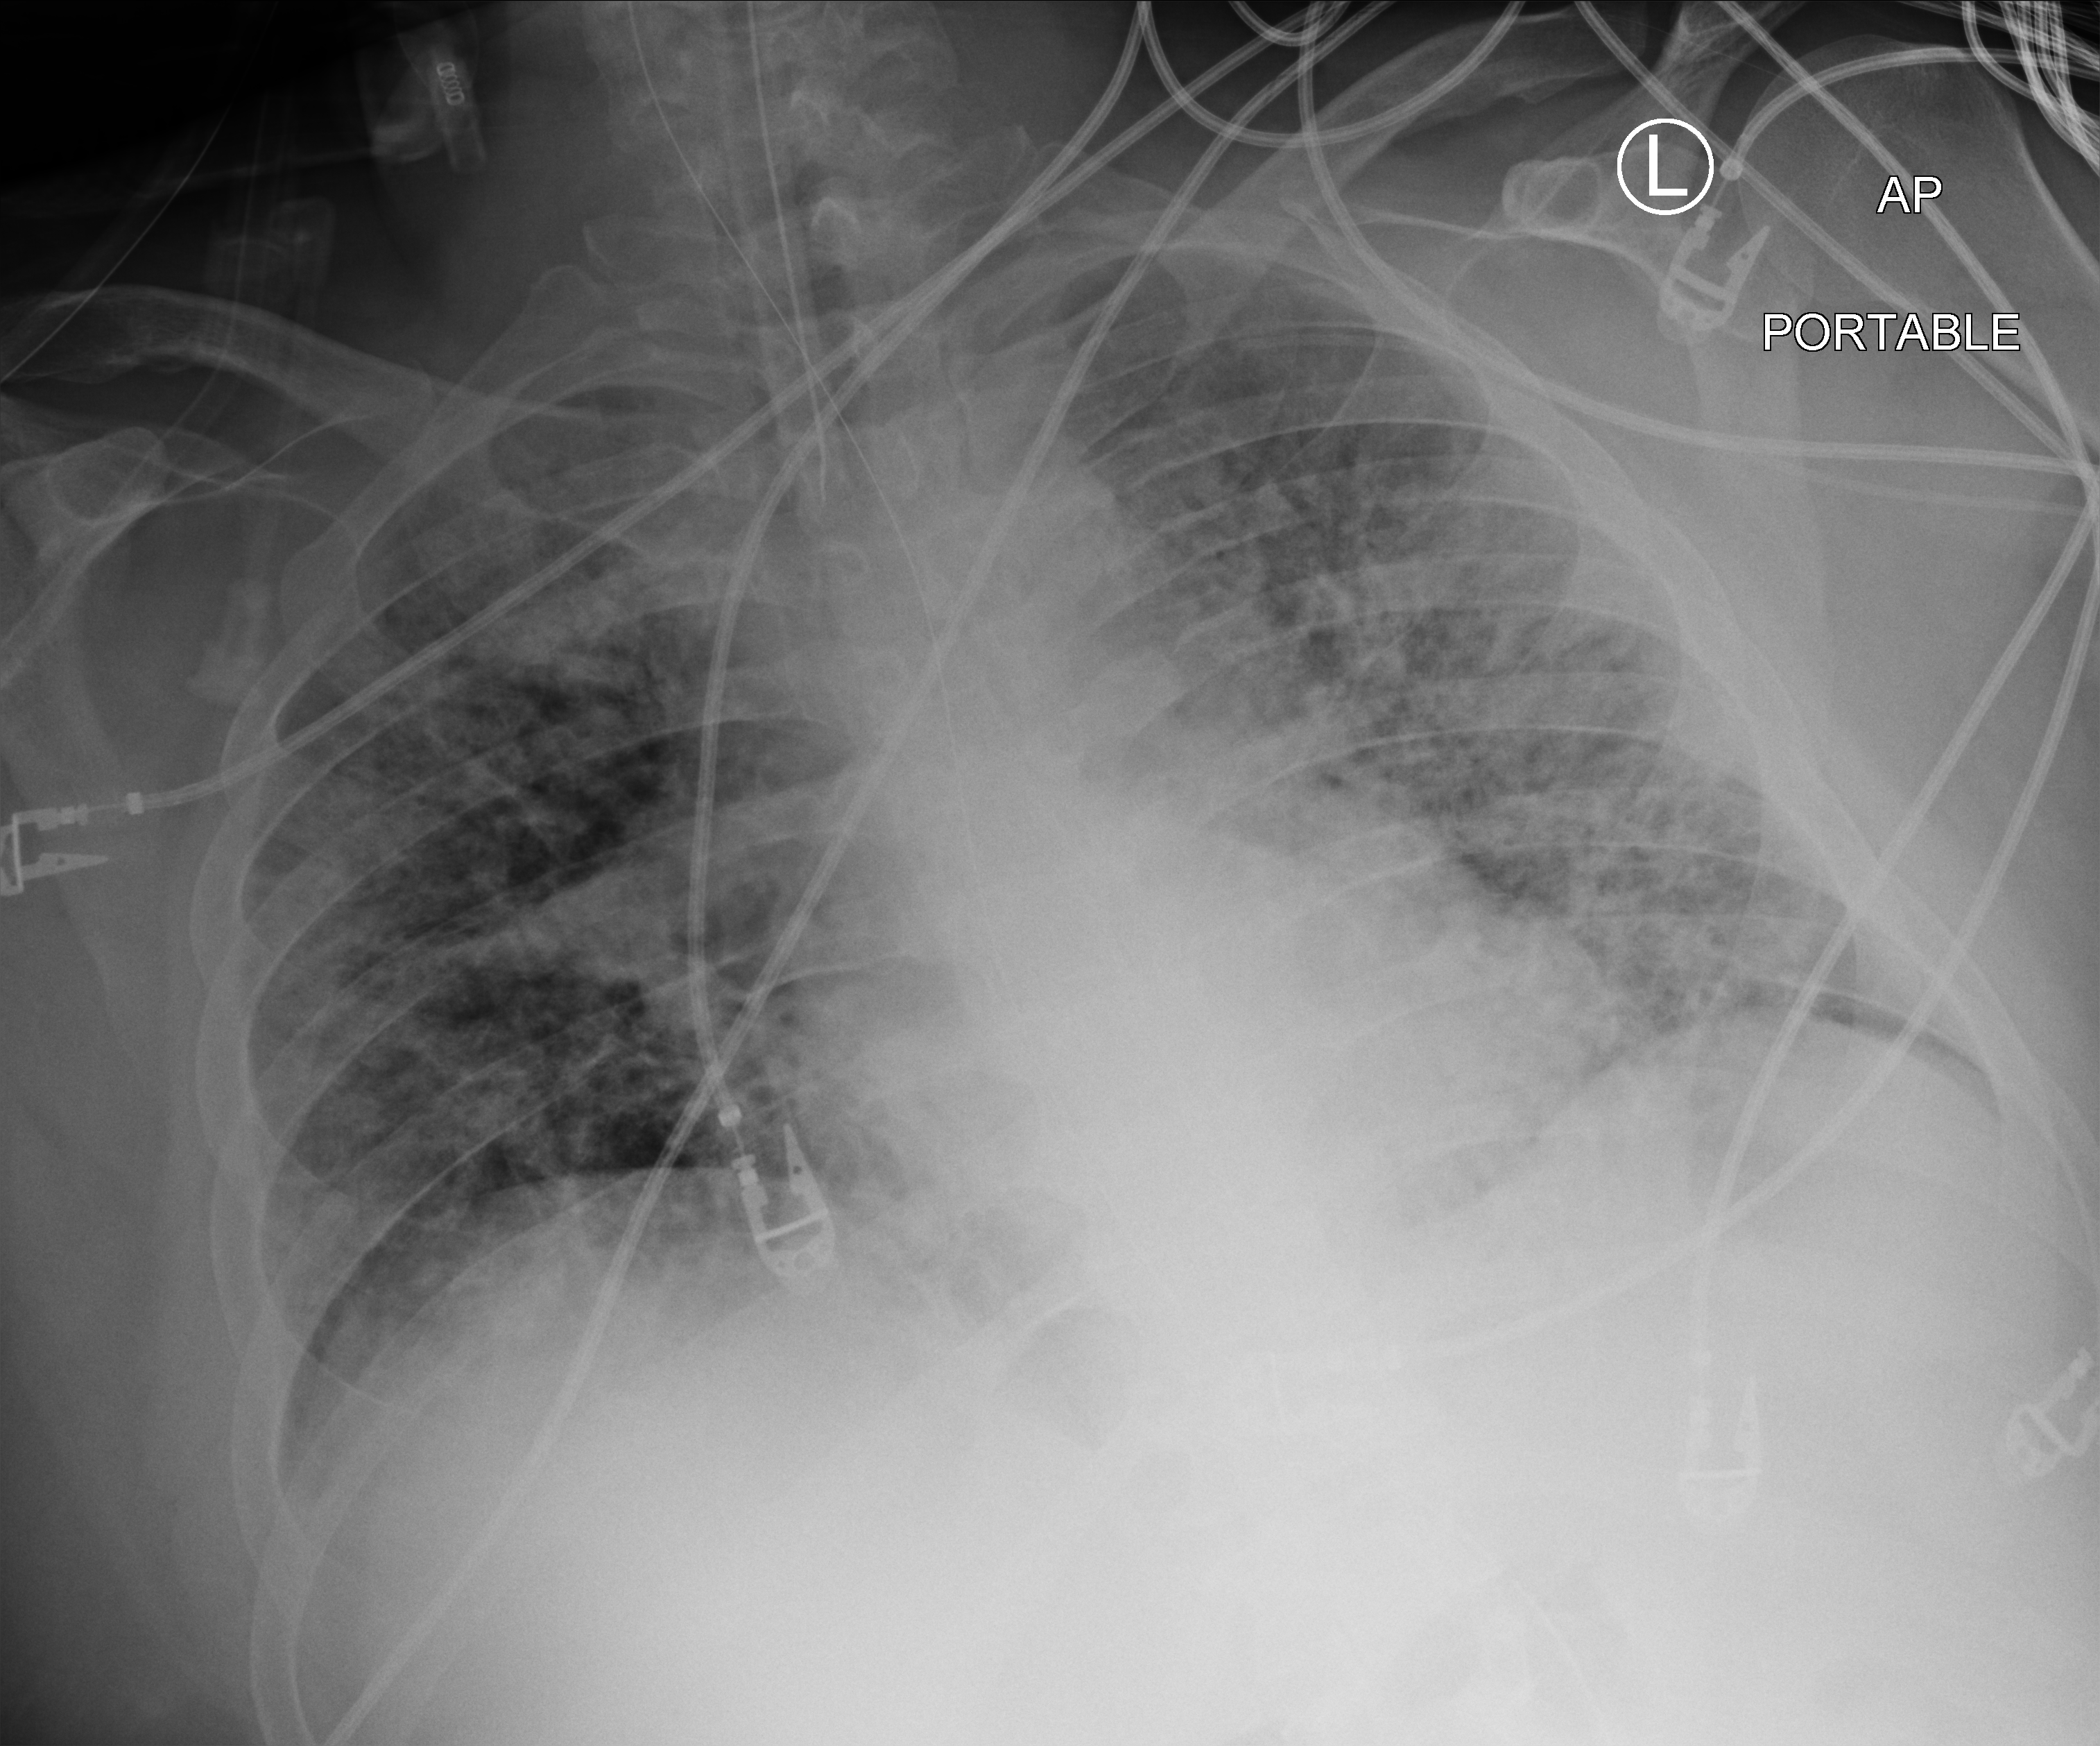
Chest X-ray (portable), anteroposterior (AP) projection. Patient hospitalised with COVID-19, aged 18–59 years.
Admission-level facts for this patient (not findings on this image; timing relative to this image not recorded): mechanically ventilated during this hospital stay: yes; admitted to intensive care during this hospital stay: yes.